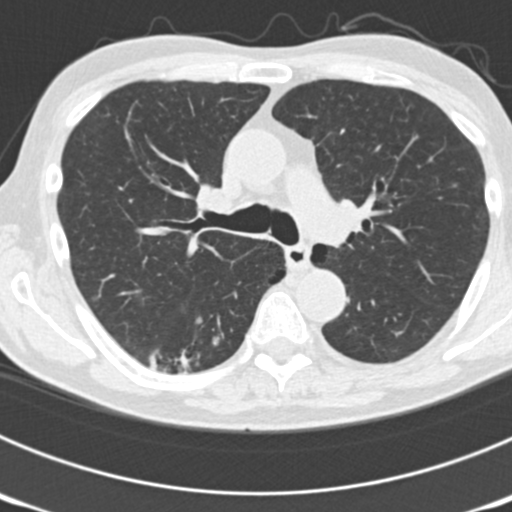
Low-dose screening chest CT, one axial slice; position 119 of 177 along the scan axis; lung window (W 1500 / L -600 HU); 2 mm slice thickness; 512 × 512 image matrix.
Structures marked on this image (manually delineated by an expert):
- lesion 6 (nodule, lower lobe of right lung): box from (x=207, y=332) to (x=224, y=349) px